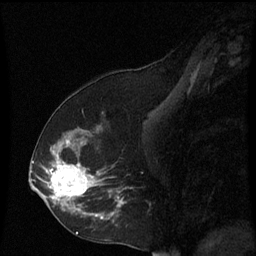
Breast MRI (dynamic contrast-enhanced), one sagittal slice; slice 35 of 60 in the series (ordered by position); dynamic contrast-enhanced series, image 2 of 3 at this slice position (ordered by acquisition); 1.5 T; TE 4.2 ms, TR 8.9 ms; 2 mm slice thickness; 256 × 256 image matrix. Female patient, age 53 years. From the clinical record (not read from this slice): setting: breast cancer imaged before/during neoadjuvant chemotherapy; receptor status: HR-positive, HER2-negative.
Outlined on this slice (semi-automatic segmentation, software-assisted and operator-edited):
- analysis volume of interest (the breast-tissue region the enhancement analysis was run in; not a lesion): bounding box (x1, y1, x2, y2) in pixels: (38, 128, 127, 231)
- tumour enhancement mask (voxels above the 70 % enhancement threshold inside the analysis volume of interest): (48, 140, 125, 219)